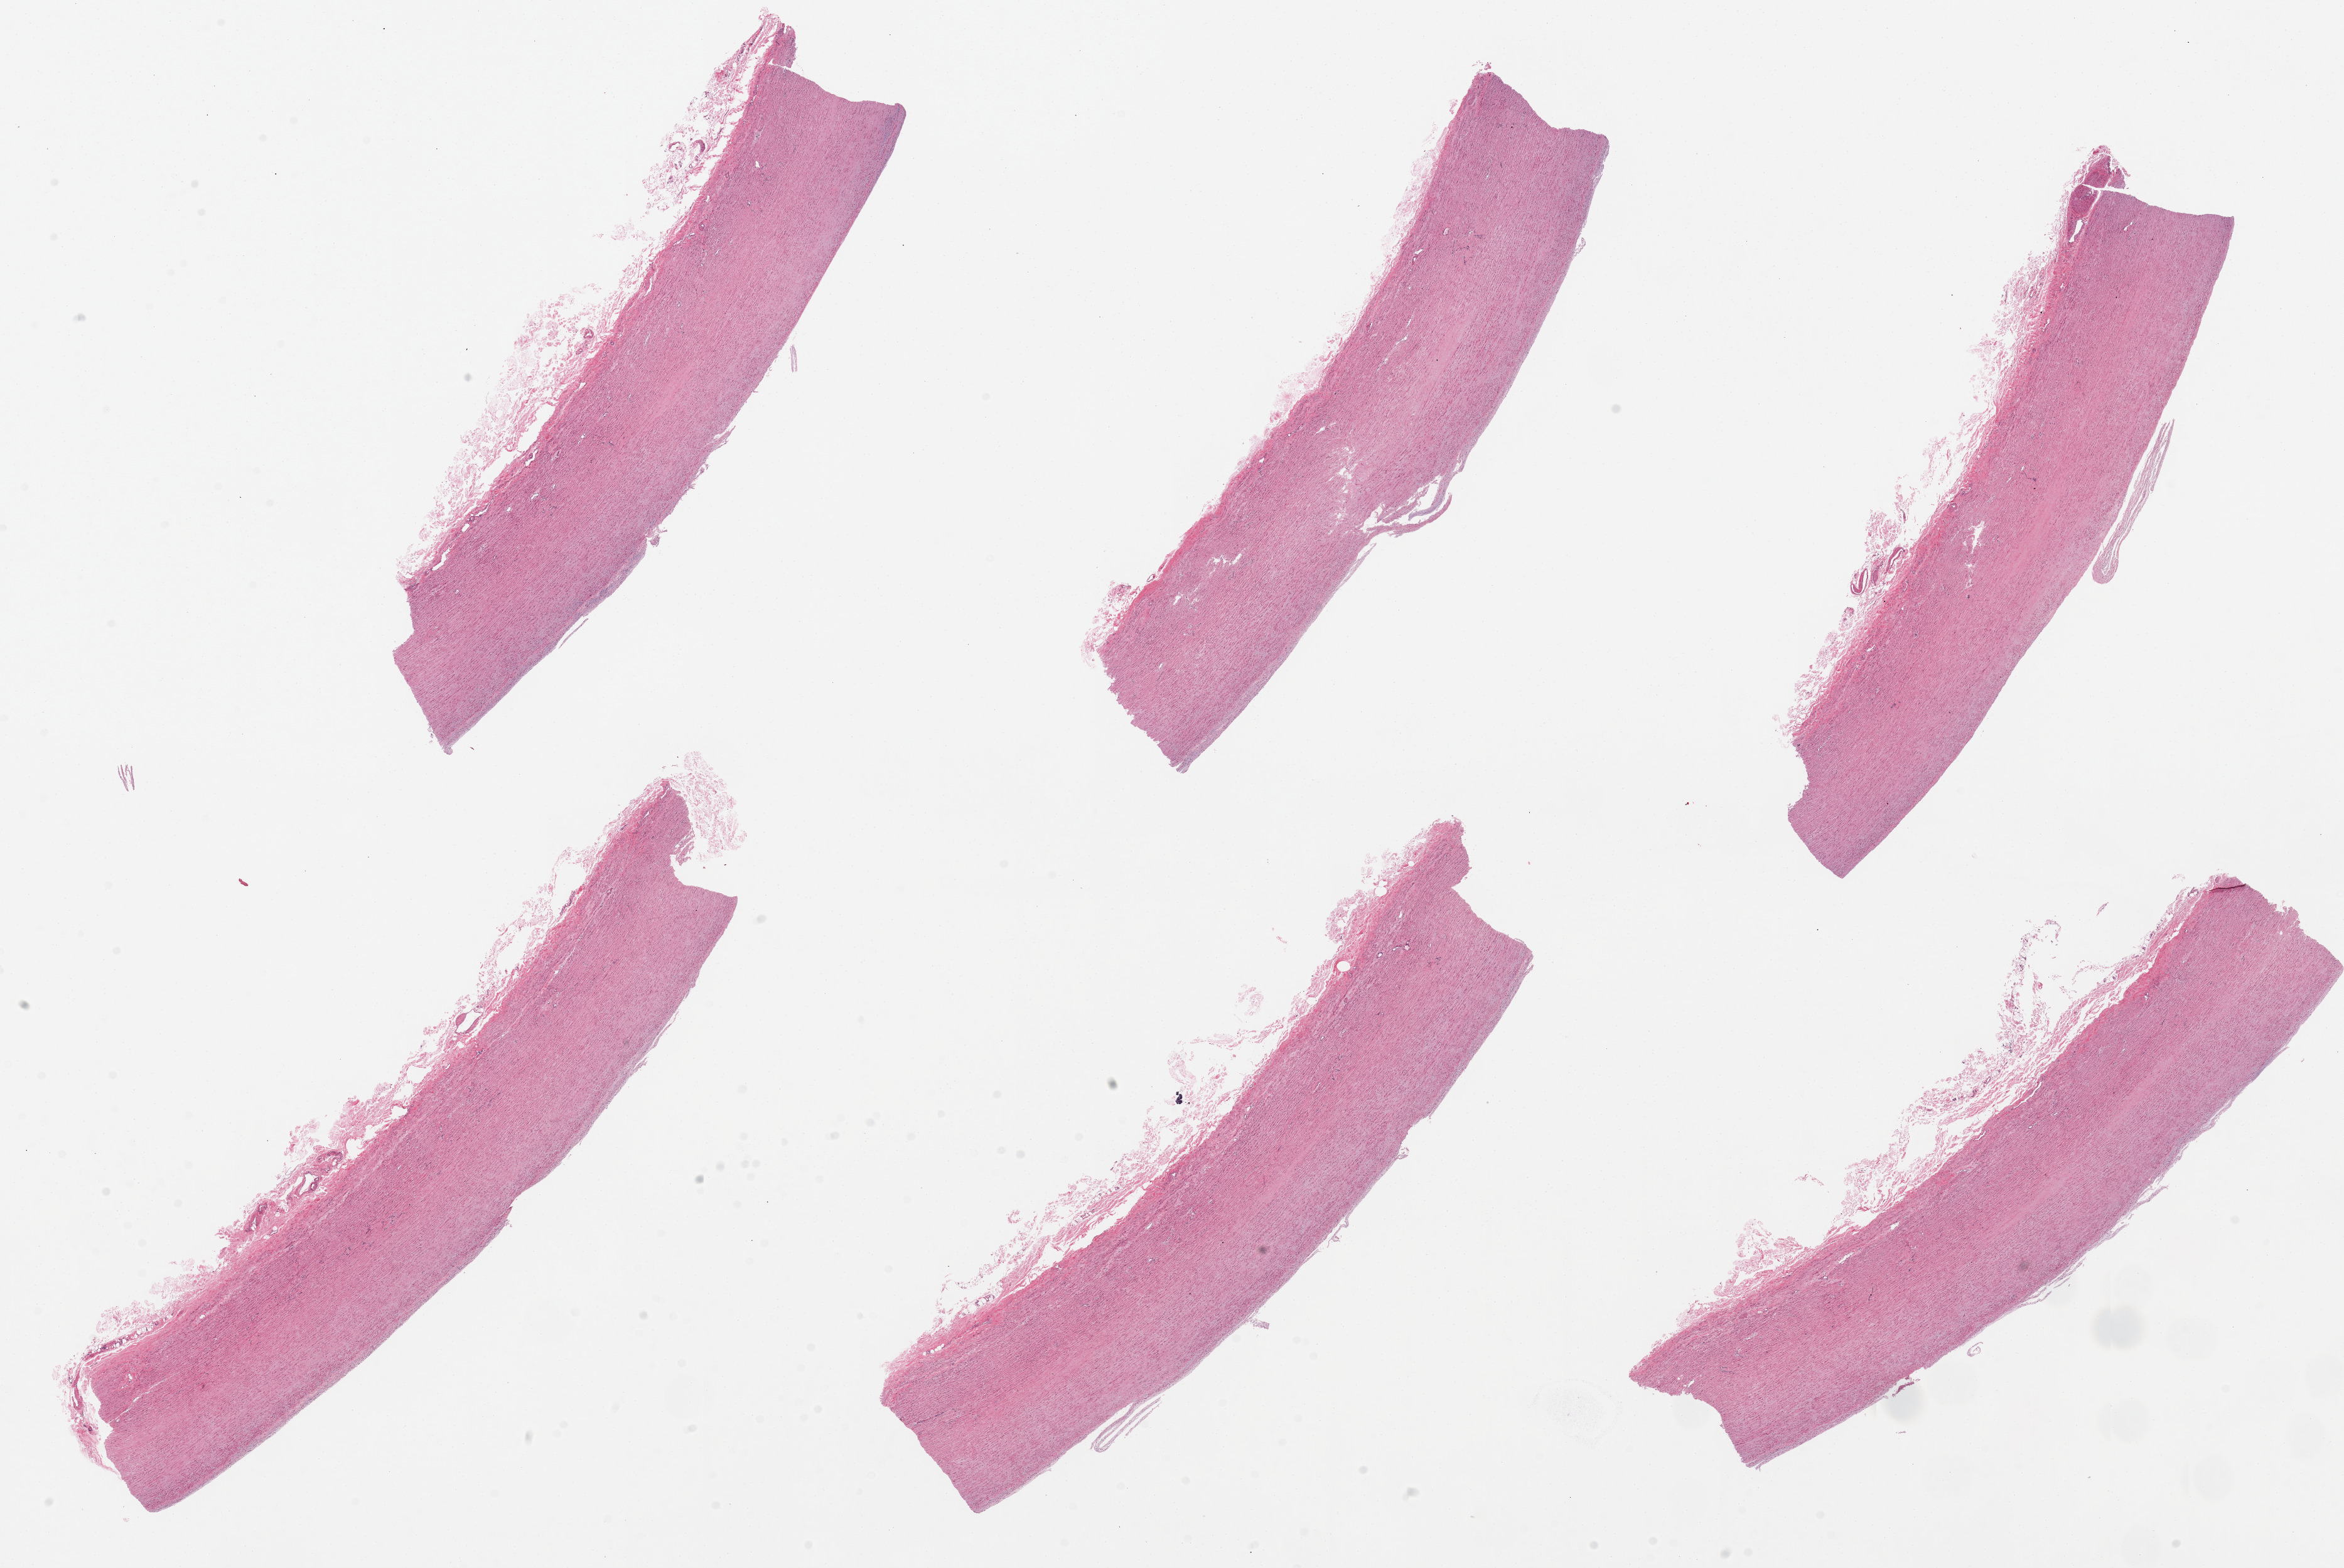
Haematoxylin and eosin whole-slide image, brightfield — whole scanned area (about 29.5 x 19.8 mm) shown as a low-resolution overview; PAXgene-fixed, paraffin-embedded tissue; target tissue: aorta; donor tissue sample. Donor: female.
Review note (as recorded): 6 pieces, up to 11x3mm. Well trimmed. No plaques.